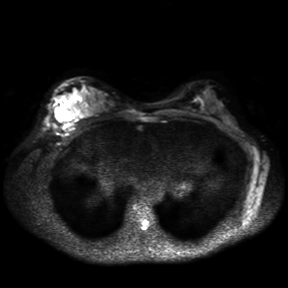
Breast MRI, one axial slice. Slice 21 of 30 in the series (ordered by position). Diffusion-weighted series; image 2 of 4 stored at this slice position (different b-values; order by instance number). 3 T. 4 mm slice thickness. 288 × 288 image matrix, field of view 360 × 360 mm. Female patient.
Outlined on this slice (manually delineated by an expert):
- tumour on diffusion-weighted imaging: bounding box (x1, y1, x2, y2) in pixels: (54, 108, 66, 122)